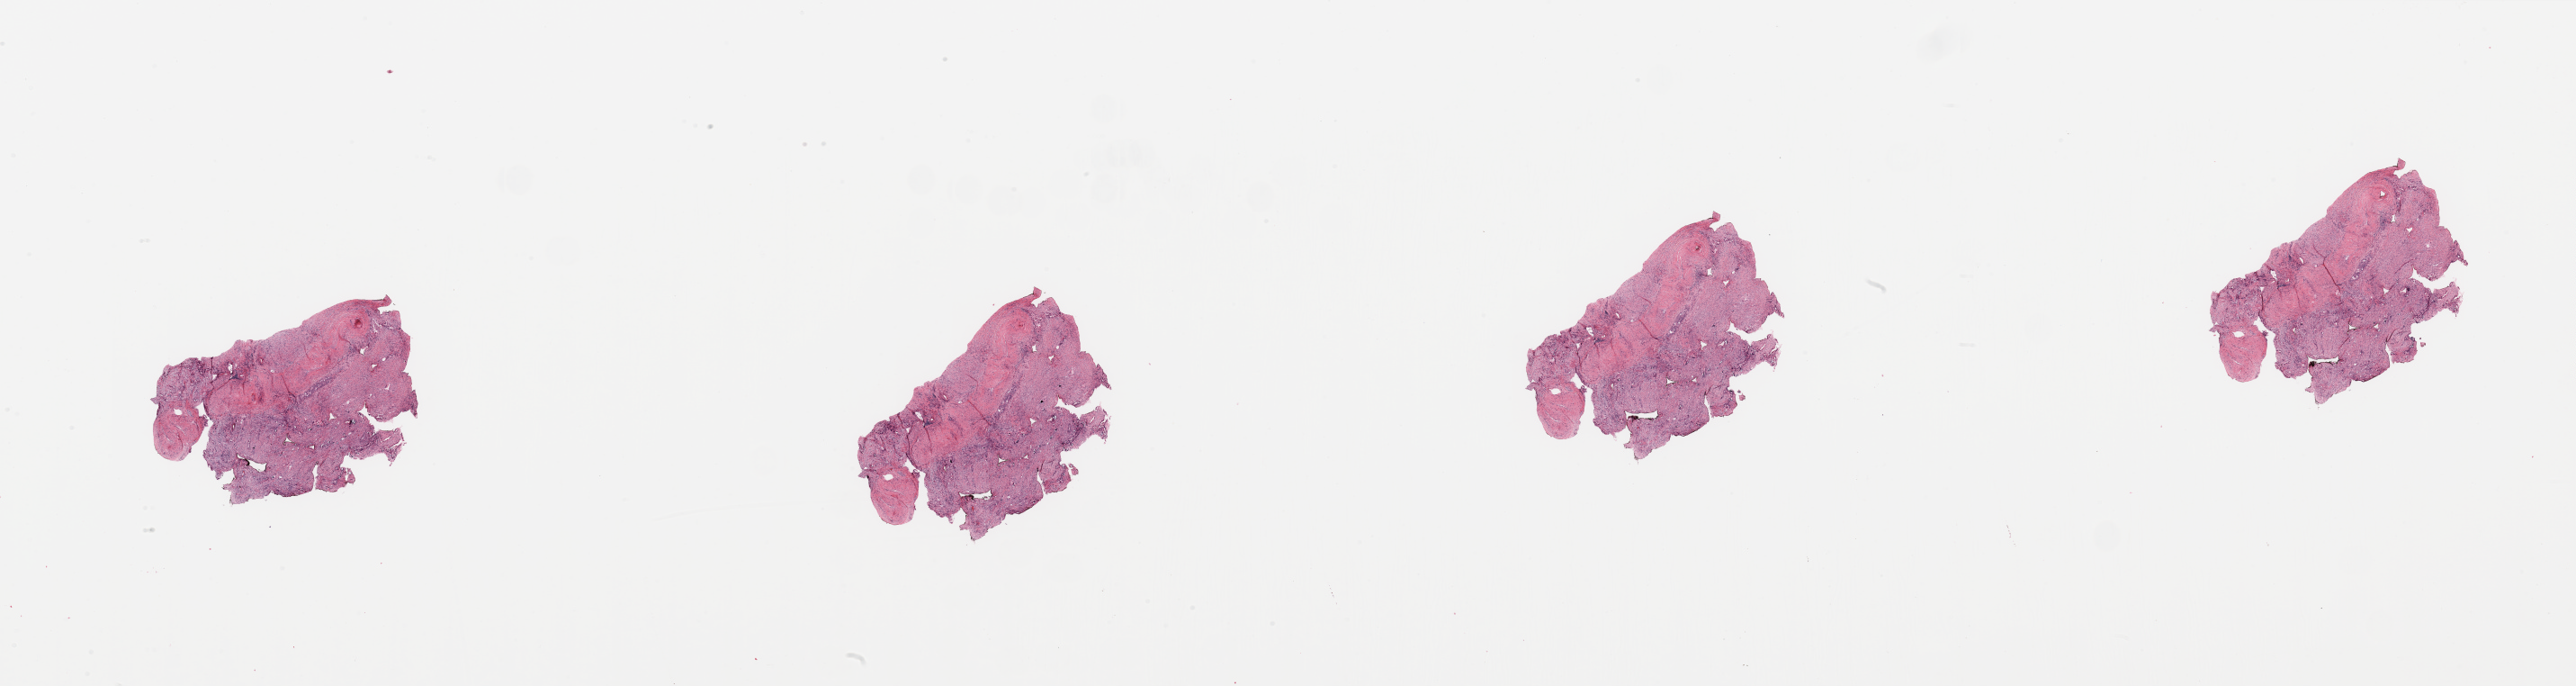
H&E-stained whole-slide image, shown as a low-resolution overview of the whole scanned area (about 45.3 x 12.1 mm, from a 20x scan), tumour tissue sample, sampled site: pancreas. 80-year-old male patient. Histologic grade: G2 (moderately differentiated). Pathologist review of this section (percent, as recorded): tumour nuclei 20%, necrosis 0%.
* primary tumour site (as recorded): head
* histologic diagnosis: Infiltrating duct carcinoma, NOS
* AJCC pathologic stage: IIA